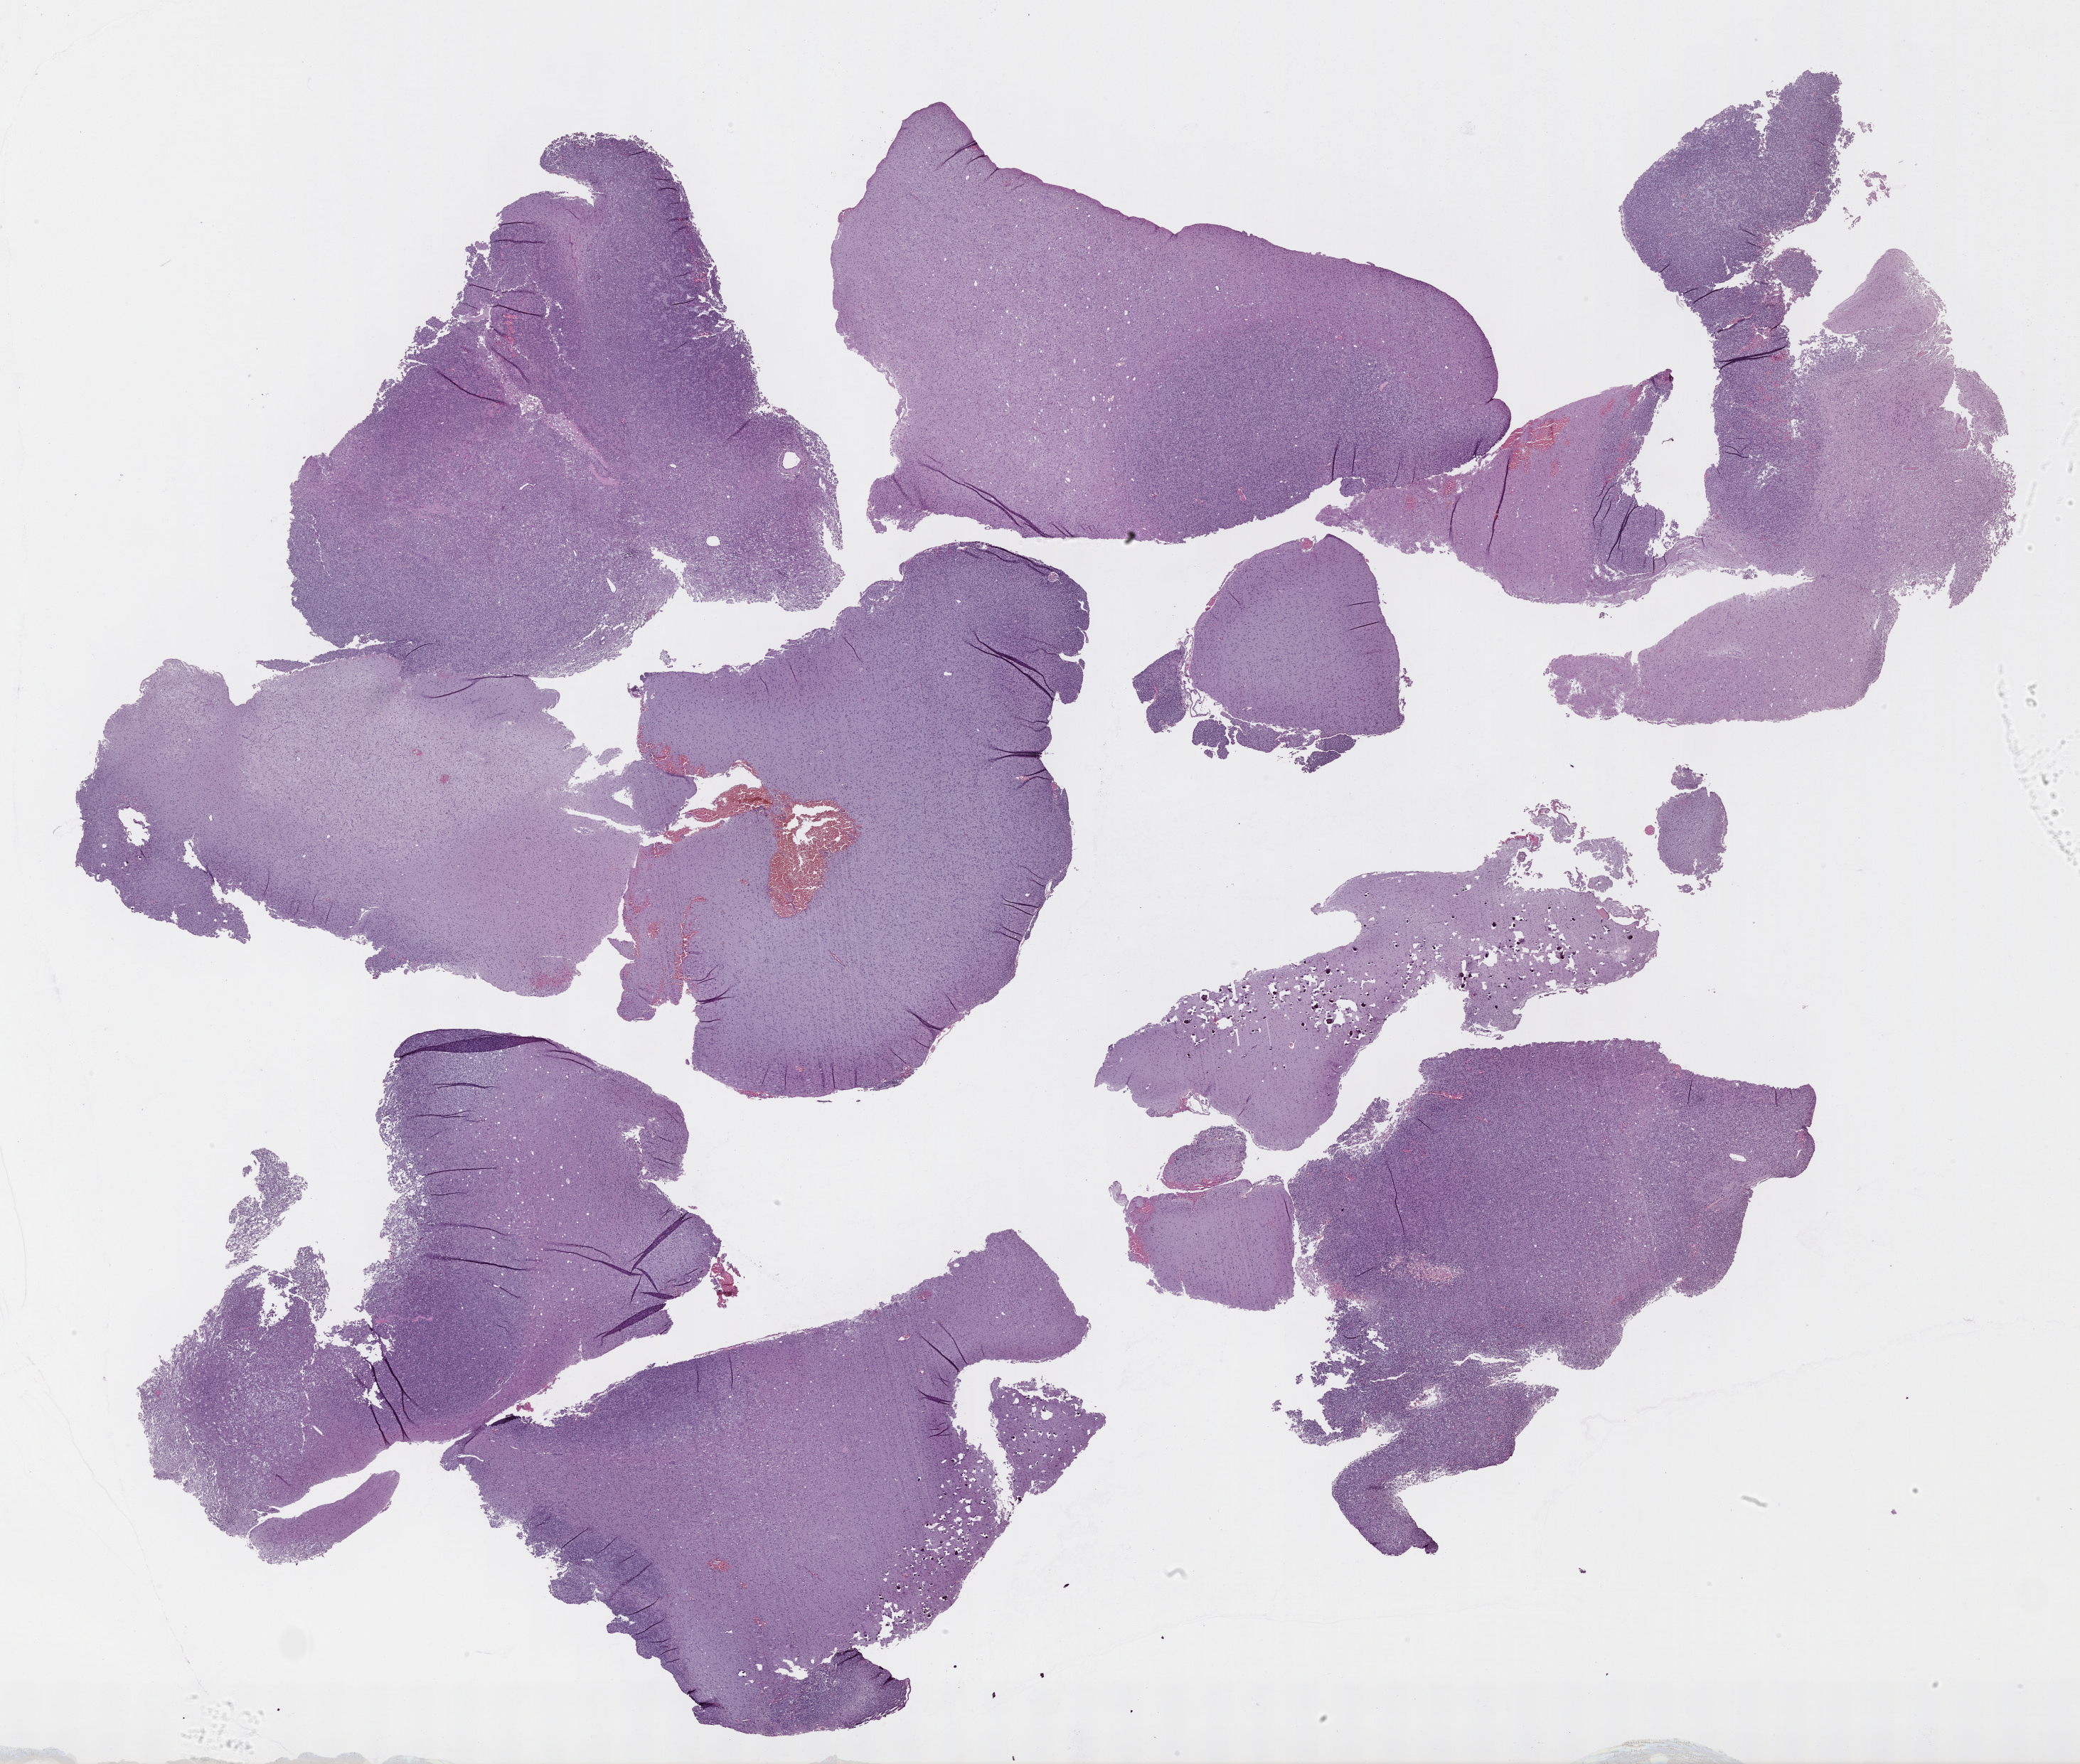
H&E-stained whole-slide image, shown as a low-resolution overview of the whole scanned area (about 23.6 x 20.1 mm). Formalin-fixed paraffin-embedded (FFPE) diagnostic section. Sample: primary tumour, brain. Female, age 37 years at initial diagnosis.
Pathologic diagnosis: Mixed glioma (cerebrum).